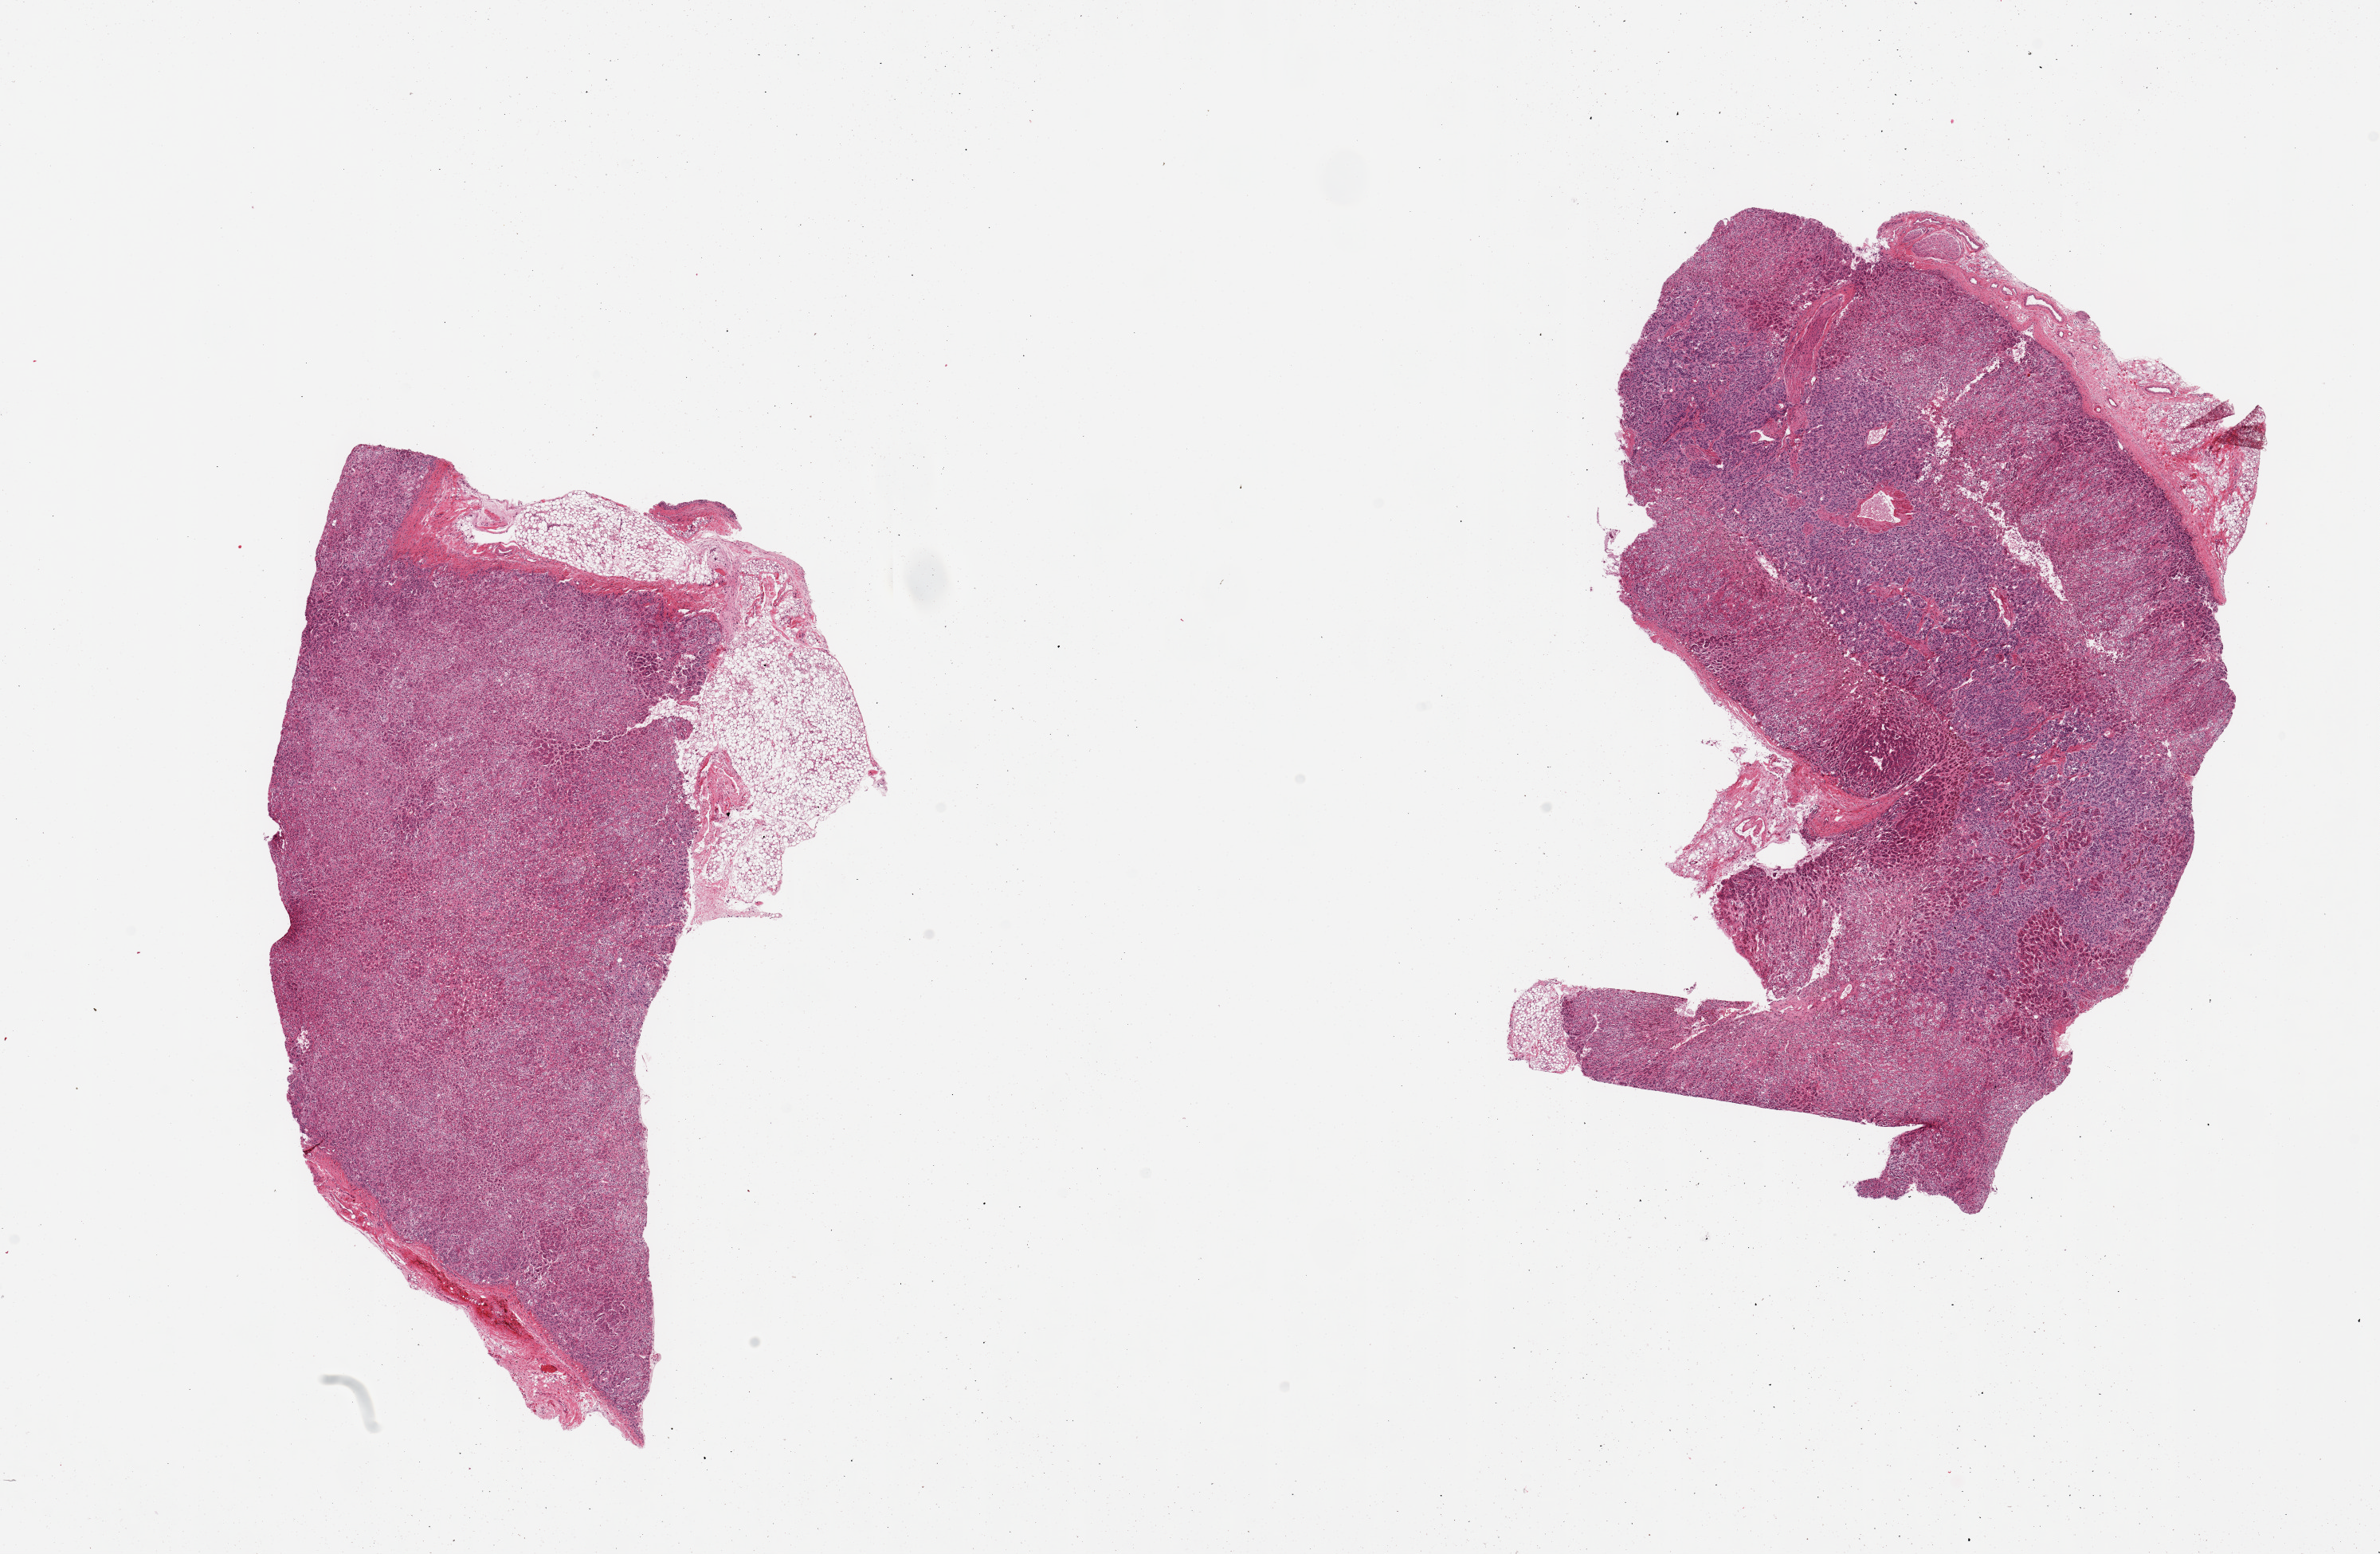
H&E whole-slide image, low-resolution overview of the scanned area, about 23.6 x 15.4 mm (from a 20x scan); PAXgene-fixed paraffin-embedded (PFPE) section; target tissue: adrenal gland; donor tissue sample. Donor sex: male.
Reviewer comment on this tissue sample: 2 pieces; 20 & 5% external fat content.